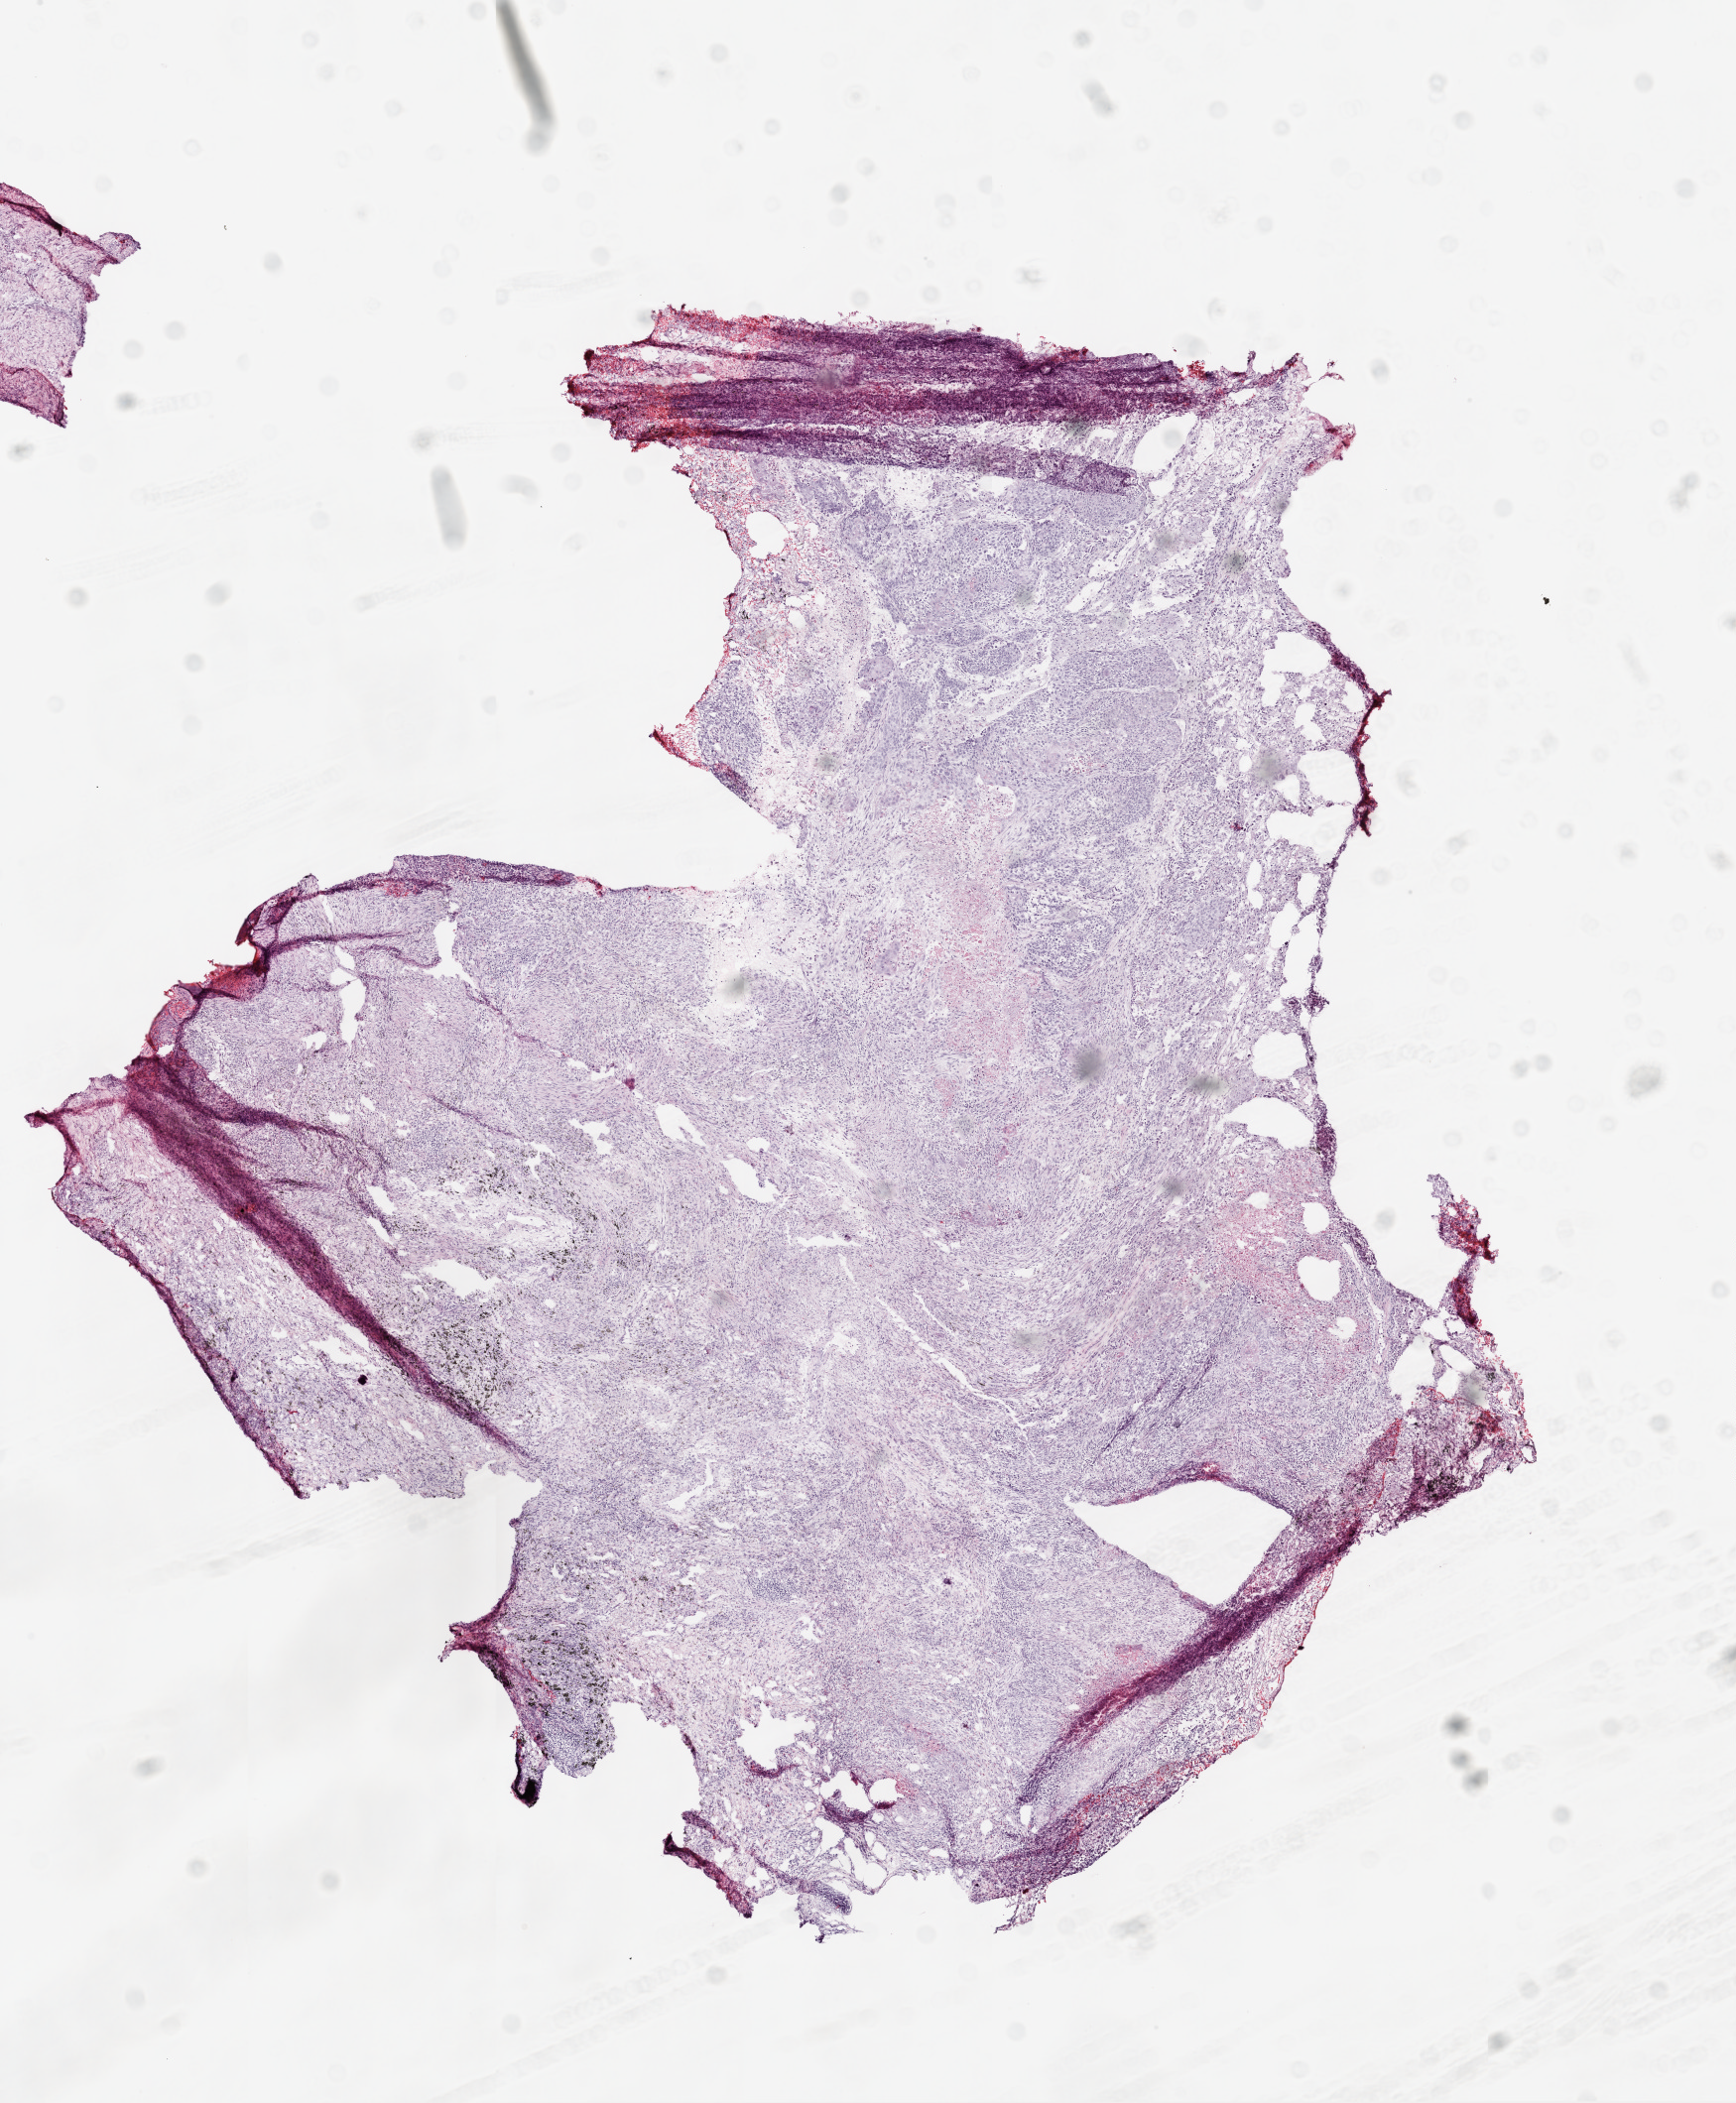
Whole-slide histology image, Hematoxylin and eosin (H&E) stained — shown as a low-resolution overview of the whole scanned area (about 7.0 x 8.5 mm, acquisition: 20x scan), frozen section, primary tumour sample from the lung. Male patient; age at initial diagnosis 51 years. Composition of this section per pathologist review: tumour cells 67%, tumour nuclei 75%, normal cells 20%, stromal cells 10%, necrosis 3%.
- TNM: T1 N0 M0
- pathologic diagnosis: Squamous cell carcinoma, NOS (upper lobe, lung)
- AJCC pathologic stage: IA (6th edition)